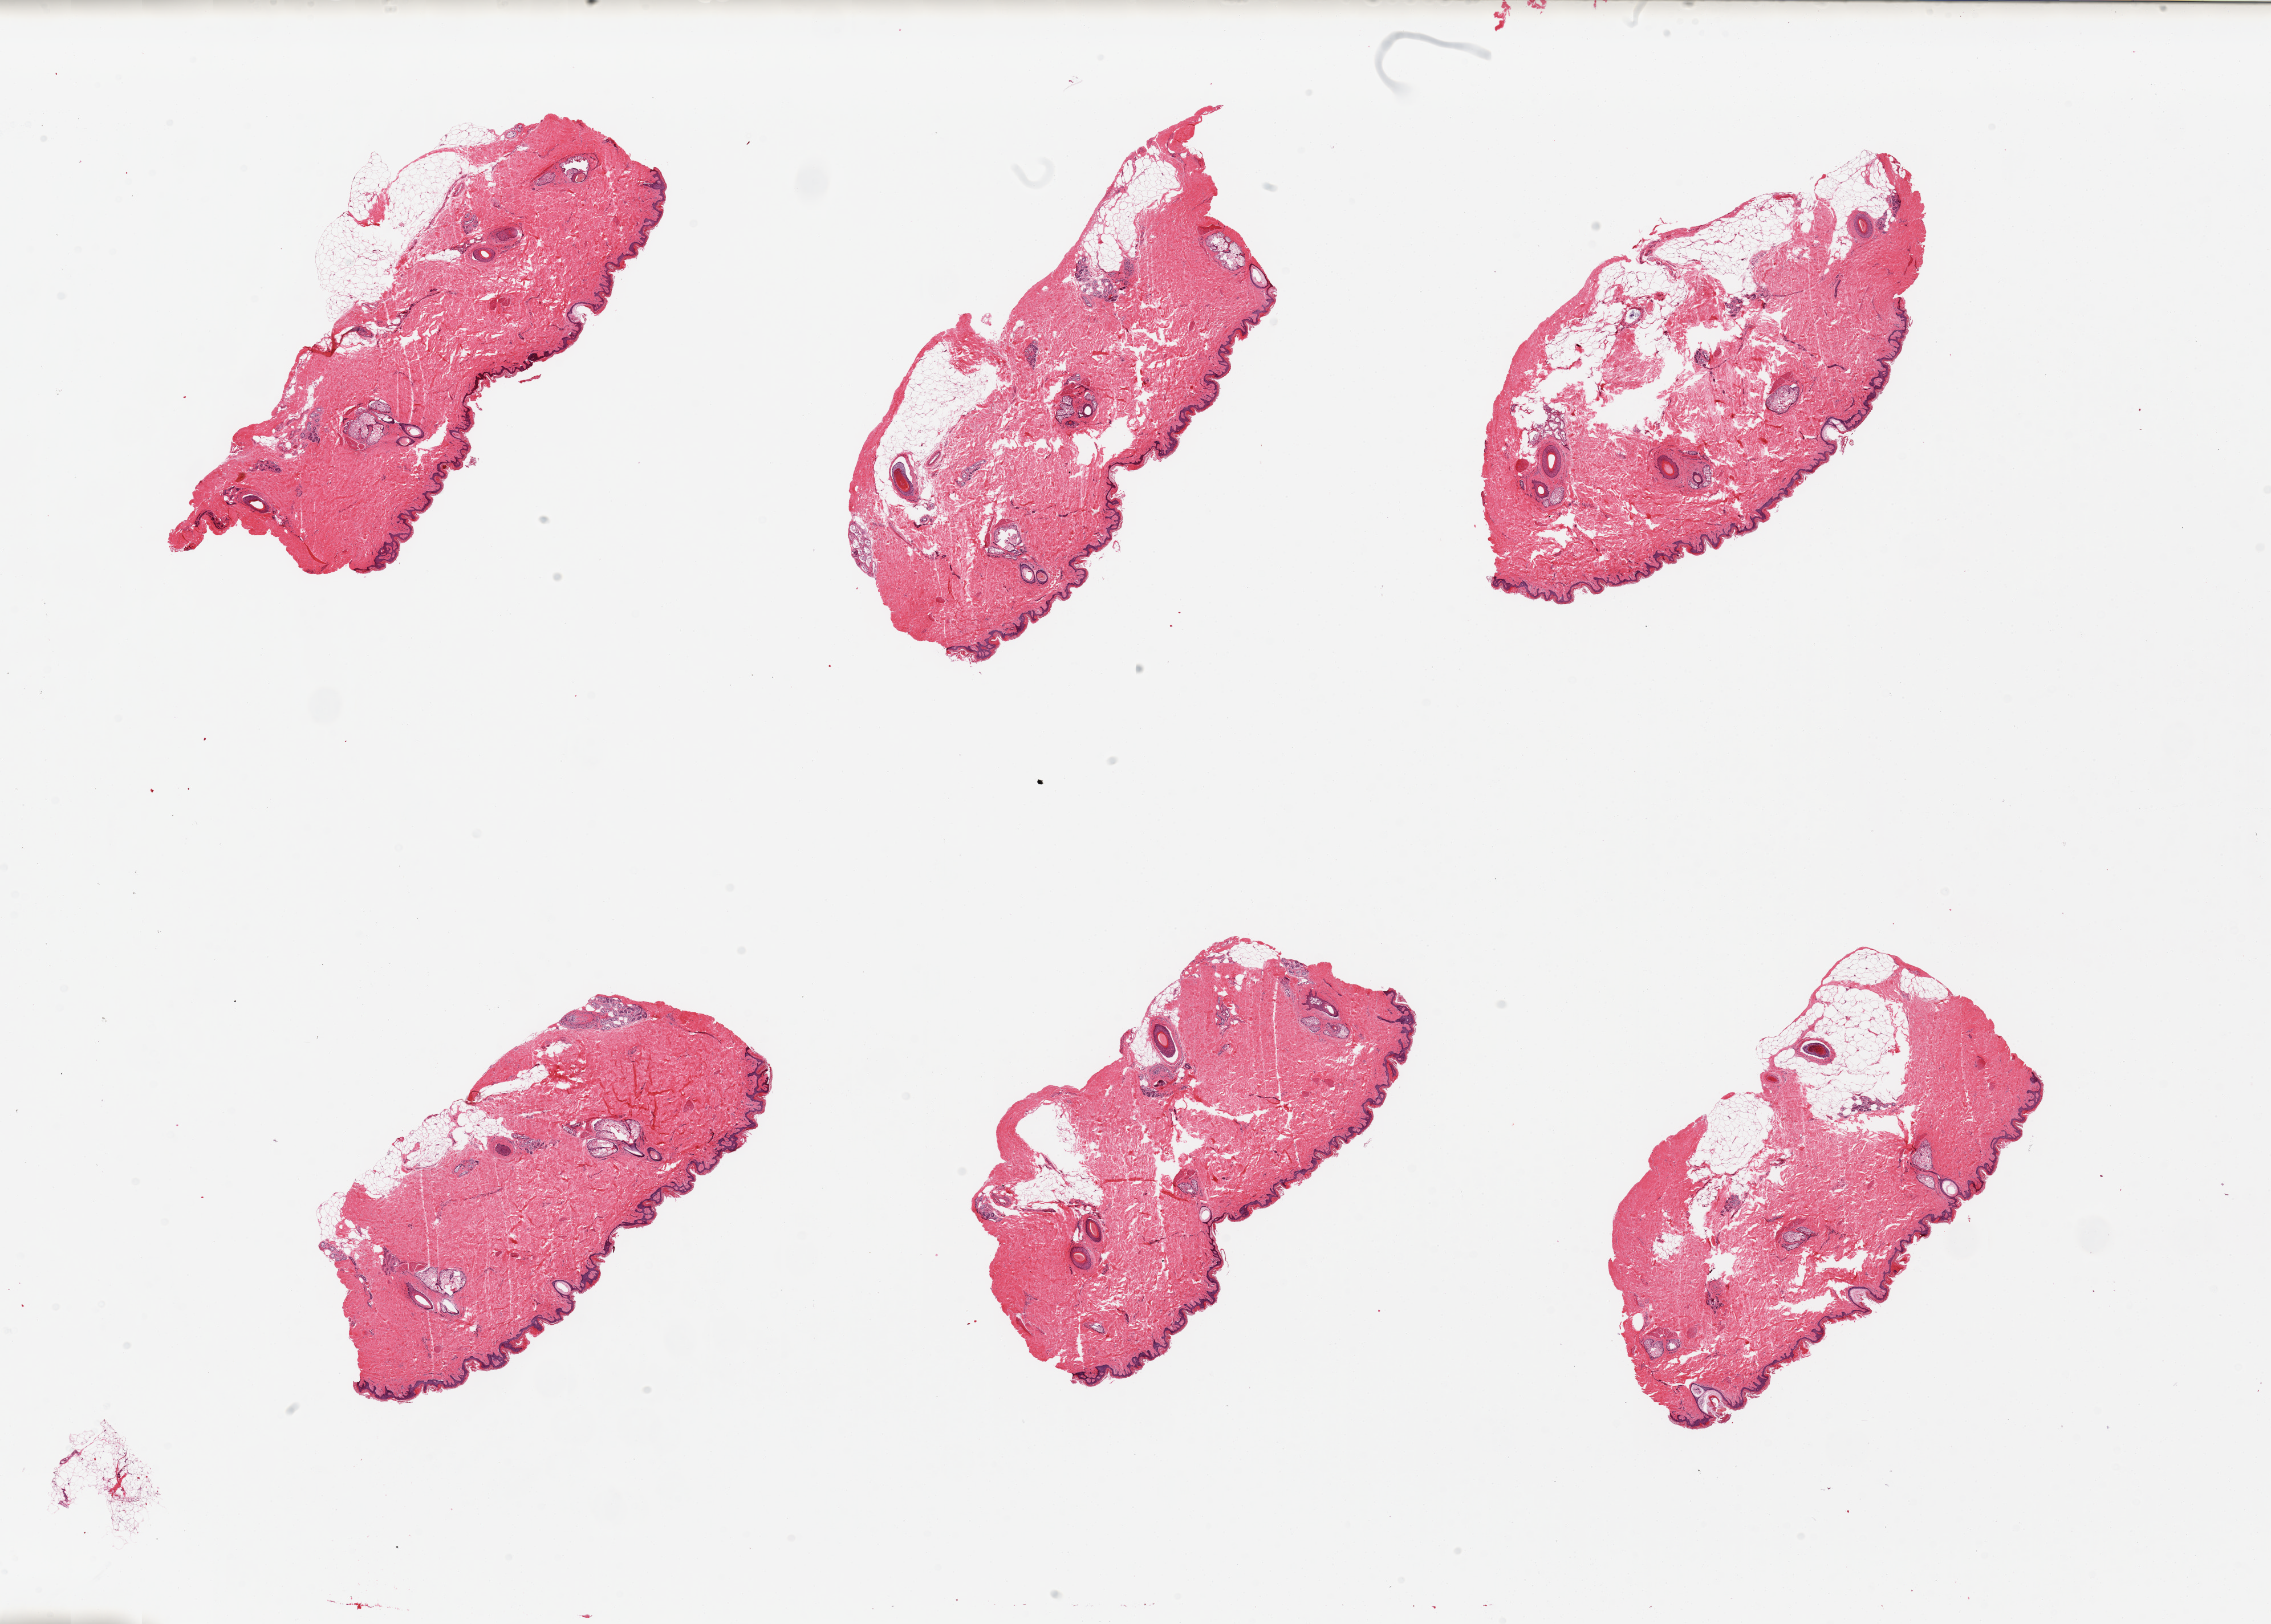
Digitized hematoxylin and eosin (H&E)-stained section, low-resolution overview of the scanned area, about 31.5 x 22.5 mm (slide scanned at 20x); PAXgene-fixed, paraffin-embedded tissue; target tissue: skin of suprapubic region; tissue donor sample. Male donor.
Pathologist's review note for this sample: 6 pieces, adherent dermal fat on 4/6; squamous epithelium is ~40-70 microns thick.